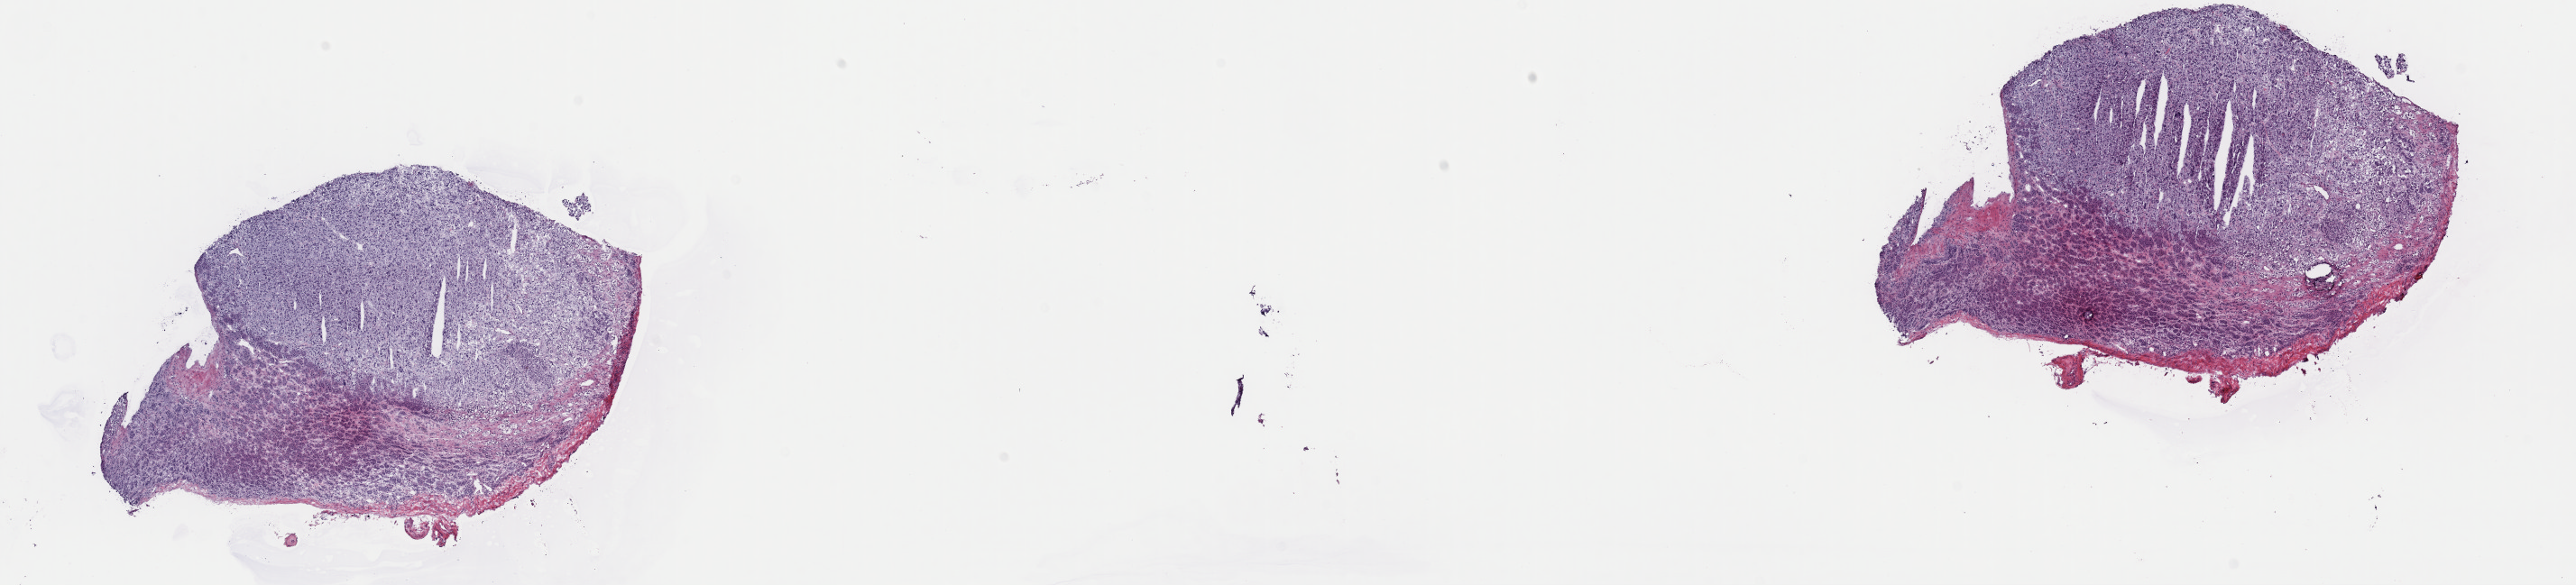
H&E-stained whole-slide image, a low-resolution overview of the entire scanned area, about 22.6 x 5.1 mm (acquisition: 40x scan); frozen section; primary tumour sample from the adrenal gland. Female patient; age at initial diagnosis 63 years. Slide review estimates, as recorded: tumour cells 50%, tumour nuclei 60%, normal cells 40%, stromal cells 10%, necrosis 0%. Inflammatory infiltration, as recorded: lymphocyte infiltration 0%, monocyte infiltration 1%, neutrophil infiltration 0%.
• diagnosis: Pheochromocytoma, malignant